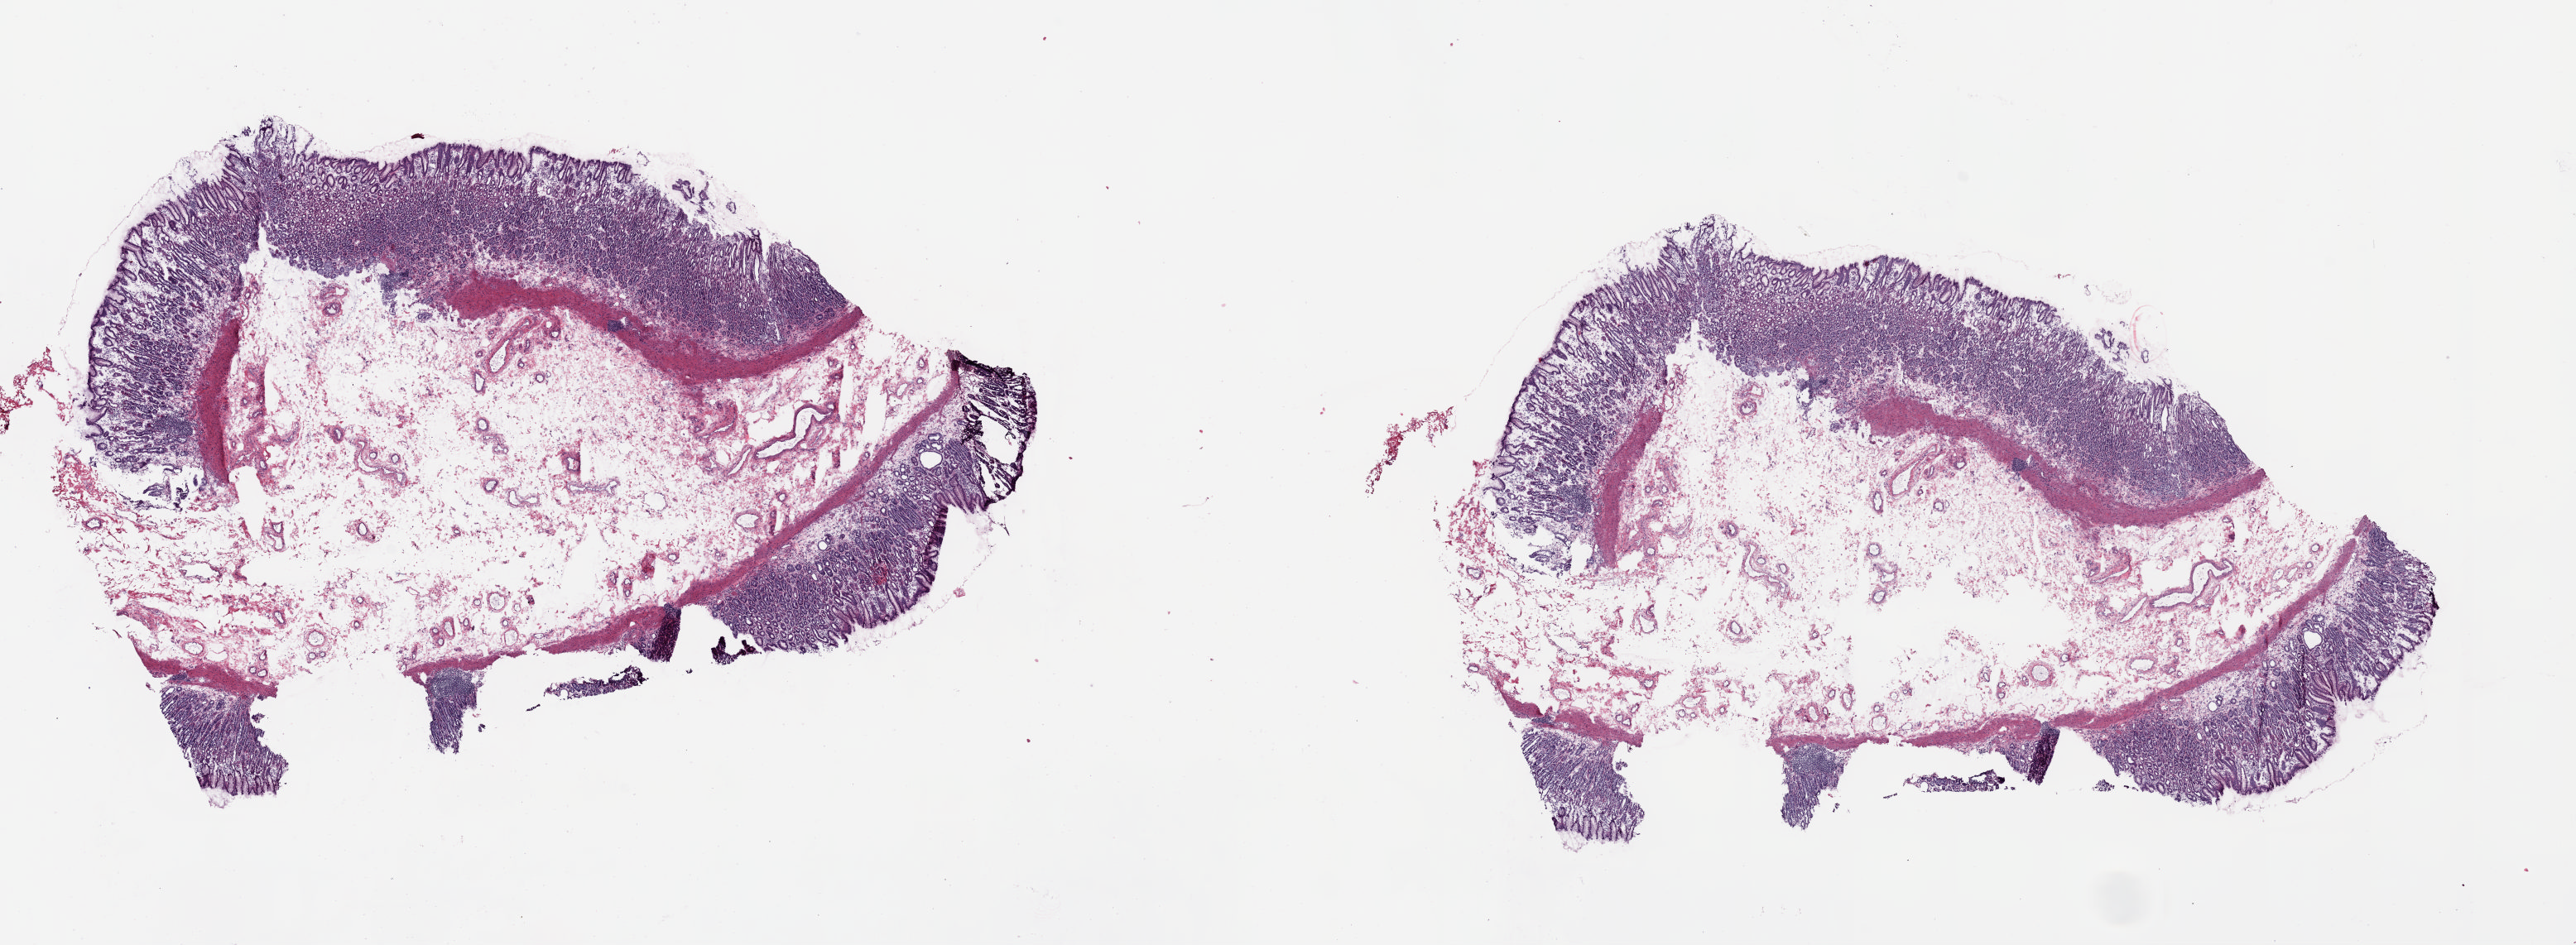
Whole-slide histology image, H&E-stained — low-resolution overview of the scanned area, about 24.5 x 9.0 mm, frozen section from the top of the tissue portion, sample: solid tissue normal (non-tumour tissue), esophagus. Male patient; age at initial diagnosis 81 years.
This section: solid tissue normal (non-tumour) sample from the same patient. Patient diagnosis: Adenocarcinoma, NOS.